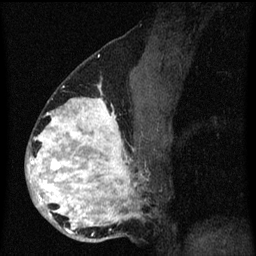
Breast MRI (dynamic contrast-enhanced), one sagittal slice; position 35 of 60 along the scan axis; dynamic contrast-enhanced series, image 2 of 3 at this slice position (ordered by acquisition); 1.5 T; TE 4.2 ms, TR 8.4 ms; 2 mm slice thickness; 256 × 256 image matrix, field of view 180 × 180 mm. Female patient, age 34 years. Case-level facts recorded for this patient, not image findings: setting: breast cancer imaged before/during neoadjuvant chemotherapy; receptor status: HR-positive, HER2-negative.
Annotated regions visible in this slice (semi-automatic segmentation, software-assisted and operator-edited):
- analysis volume of interest (the breast-tissue region the enhancement analysis was run in; not a lesion): bounding box [x1, y1, x2, y2] px = [26, 58, 157, 243]
- tumour enhancement mask (voxels above the 70 % enhancement threshold inside the analysis volume of interest): [26, 84, 141, 235]